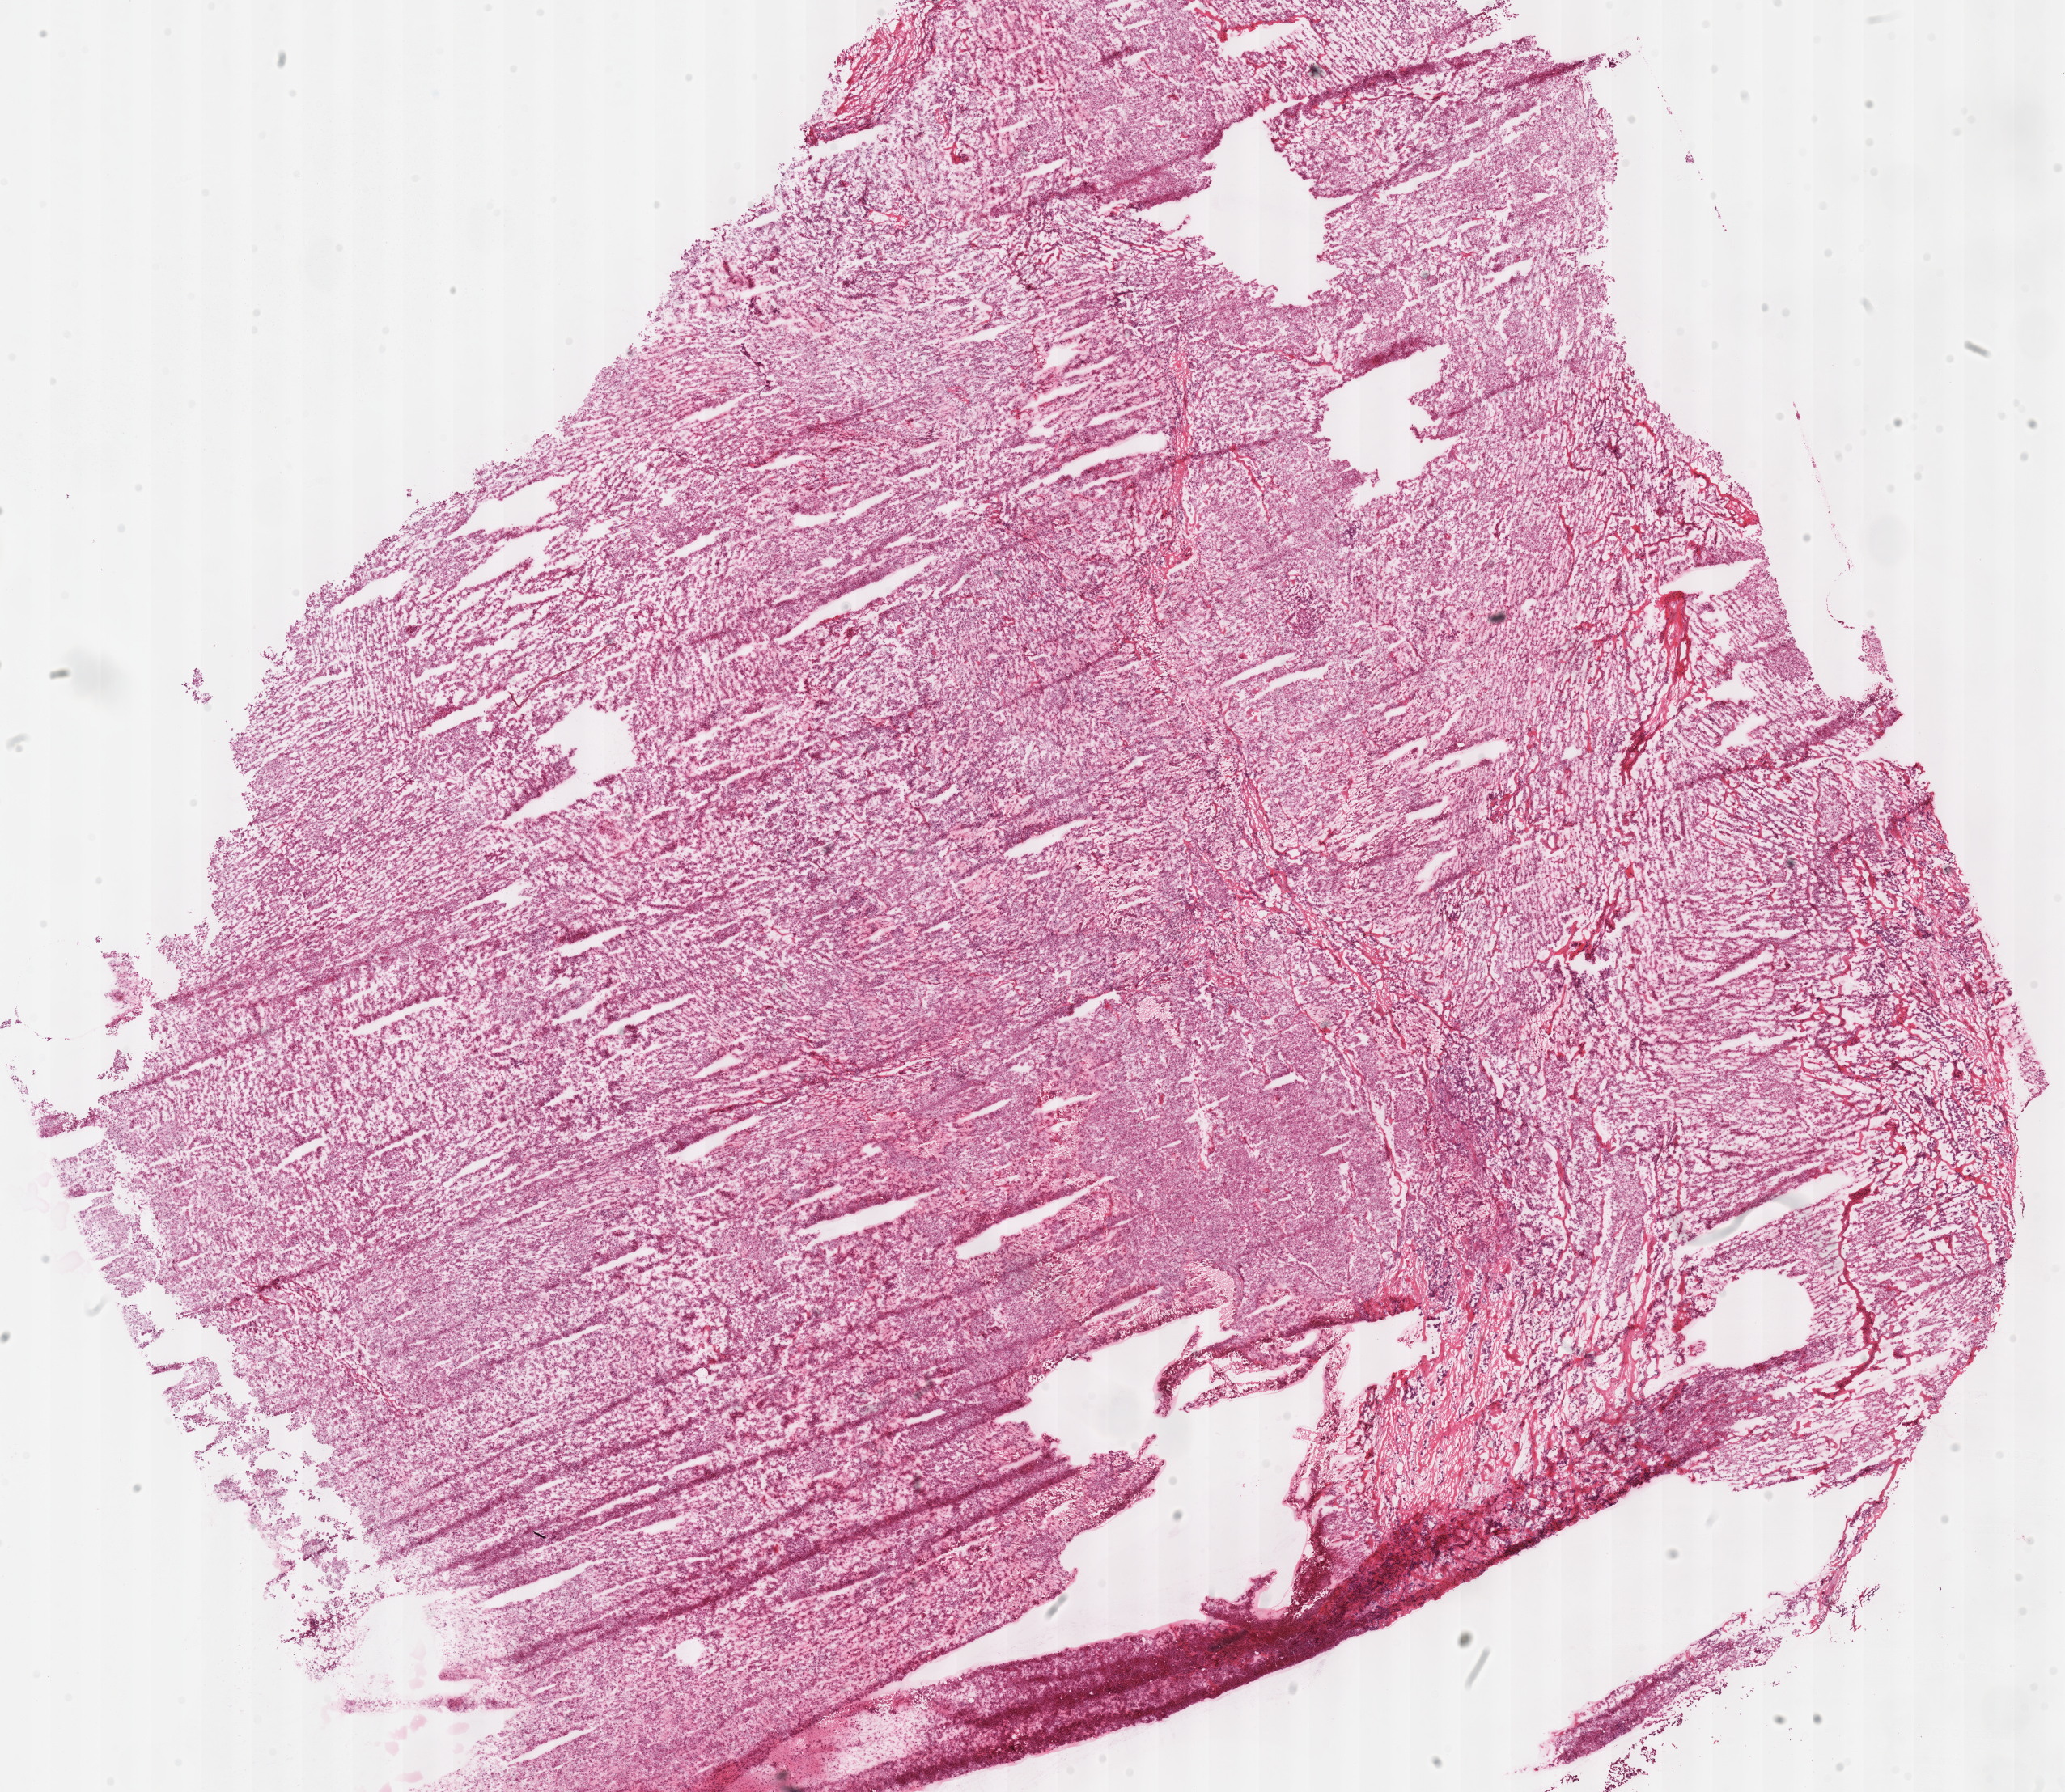
Whole-slide histology image, H&E — a low-resolution overview of the entire scanned area, about 20.1 x 17.4 mm, frozen section from the top of the tissue portion, kidney, primary tumour sample. Female, age 57 years at initial diagnosis. Composition of this section per pathologist review: tumour cells 100%, tumour nuclei 90%, normal cells 0%, stromal cells 0%, necrosis 0%. Inflammatory infiltration, as recorded: lymphocyte infiltration 1%, monocyte infiltration 0%, neutrophil infiltration 0%.
Lymph nodes positive (case pathology): 0 of 1 examined. Histologic diagnosis: Renal cell carcinoma, chromophobe type. AJCC pathologic stage: I (6th edition).